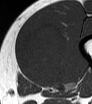
MRI of an extremity soft-tissue mass, one axial slice. MR volume resampled by the dataset authors to the PET/CT grid (not the native acquisition matrix). 3.27 mm slice thickness. 92 × 104 image matrix, field of view 90 × 102 mm. Male patient. From the clinical record (not read from this slice): histological type: mixoid liposarcoma; grade: low; site of the primary tumour: left thigh.
Outlined on this slice (expert contour drawn on MRI and transferred to this co-registered scan by the dataset authors):
- gross tumour volume (mass): bounding box (x1, y1, x2, y2) in pixels: (21, 22, 68, 84)